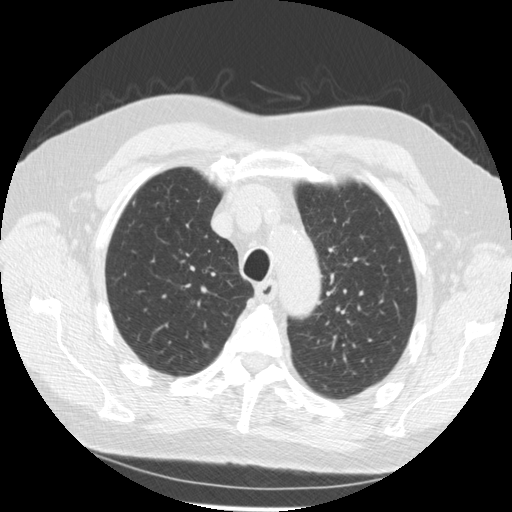
Low-dose screening chest CT, one axial slice; slice 207 of 259 in the series (ordered by position); lung window (W 1500 / L -600 HU); 2.5 mm slice thickness; 512 × 512 image matrix, field of view 355 × 355 mm.
Outlined on this slice (expert manual segmentation):
- lesion 1 (nodule, upper lobe of right lung): bounding box [x1, y1, x2, y2] px = [203, 342, 210, 349]